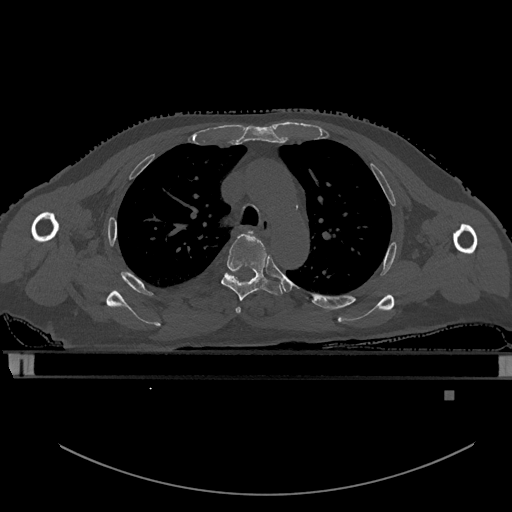
CT including the spine, one axial slice. Slice 407 of 969 in the series (ordered by position). Bone window (W 1800 / L 400 HU). 0.5 mm slice thickness. 512 × 512 image matrix, field of view 456 × 456 mm. Patient: male, 82 years. Case-level facts recorded for this patient, not image findings: primary cancer: prostate; vertebrae with lytic lesions (as recorded): T11, T9, T8, T2.
Structures marked on this image (semi-automatically segmented with operator editing):
- T3 vertebra: bounding box (x1, y1, x2, y2) in pixels: (235, 231, 251, 314)
- T4 vertebra: (221, 233, 283, 301)
- T5 vertebra: (225, 274, 233, 280)